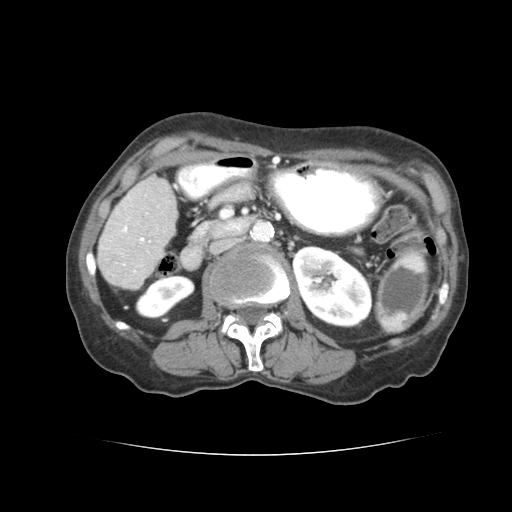
Contrast-enhanced abdominal CT (liver protocol), one axial slice. Slice 19 of 77 in the series (ordered by position). Soft-tissue window (W 400 / L 40 HU). 2.5 mm slice thickness. 512 × 512 image matrix, field of view 340 × 340 mm. From the clinical record (not read from this slice): diagnosis: hepatocellular carcinoma (patient treated with transarterial chemoembolisation; whether this scan precedes or follows treatment is not stated here); TNM stage (as recorded): Stage-I; Child-Pugh class: A; tumour nodularity: uninodular; tumour size: 7.6 cm.
Annotated regions visible in this slice (semi-automatic segmentation, software-assisted and operator-edited):
- liver parenchyma outside the tumour (the mass and vessels are separate outlines, so this box may not span the whole liver): bounding box (x1, y1, x2, y2) in pixels: (98, 176, 174, 286)
- liver vessels: (121, 192, 149, 263)